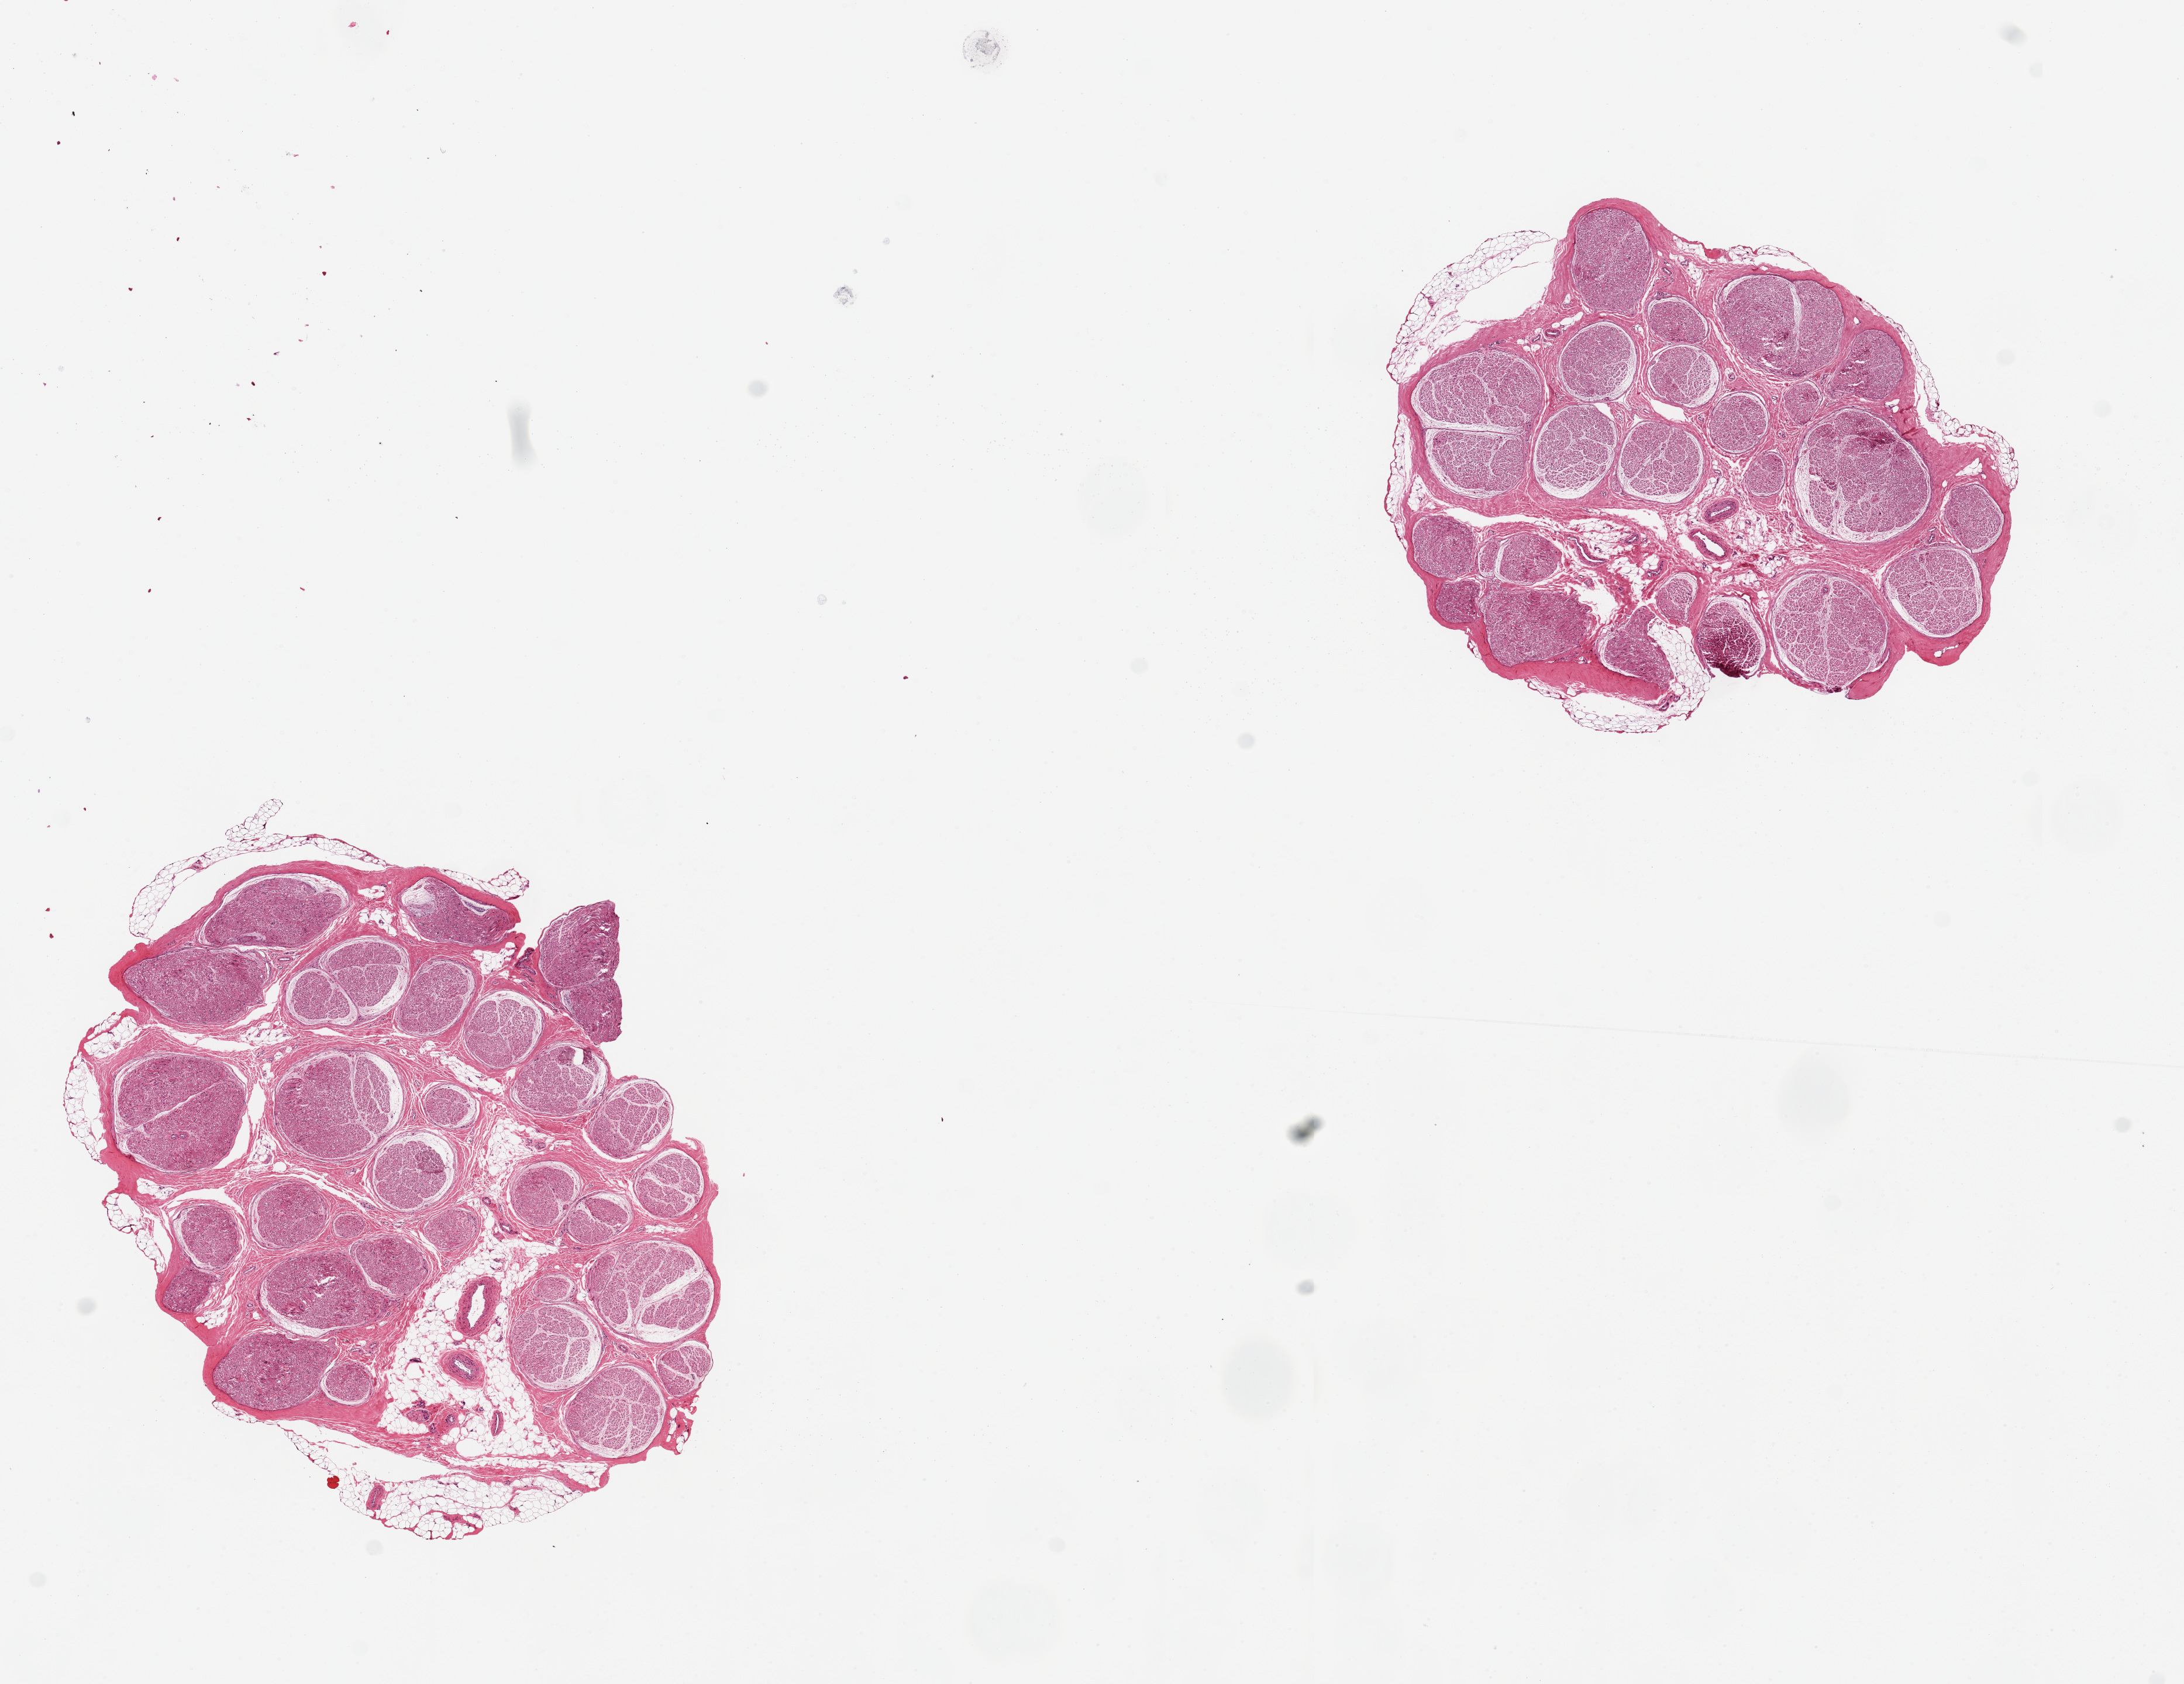
Digitized haematoxylin and eosin-stained section, shown as a low-resolution overview of the whole scanned area (about 14.8 x 11.4 mm, from a 20x scan), PAXgene-fixed, paraffin-embedded tissue, section of tibial nerve (target tissue), tissue donor sample. Donor: male.
• pathologist's review note for this sample: 2 pieces, ~4 mm fat/connective tissue <10% of total specimen